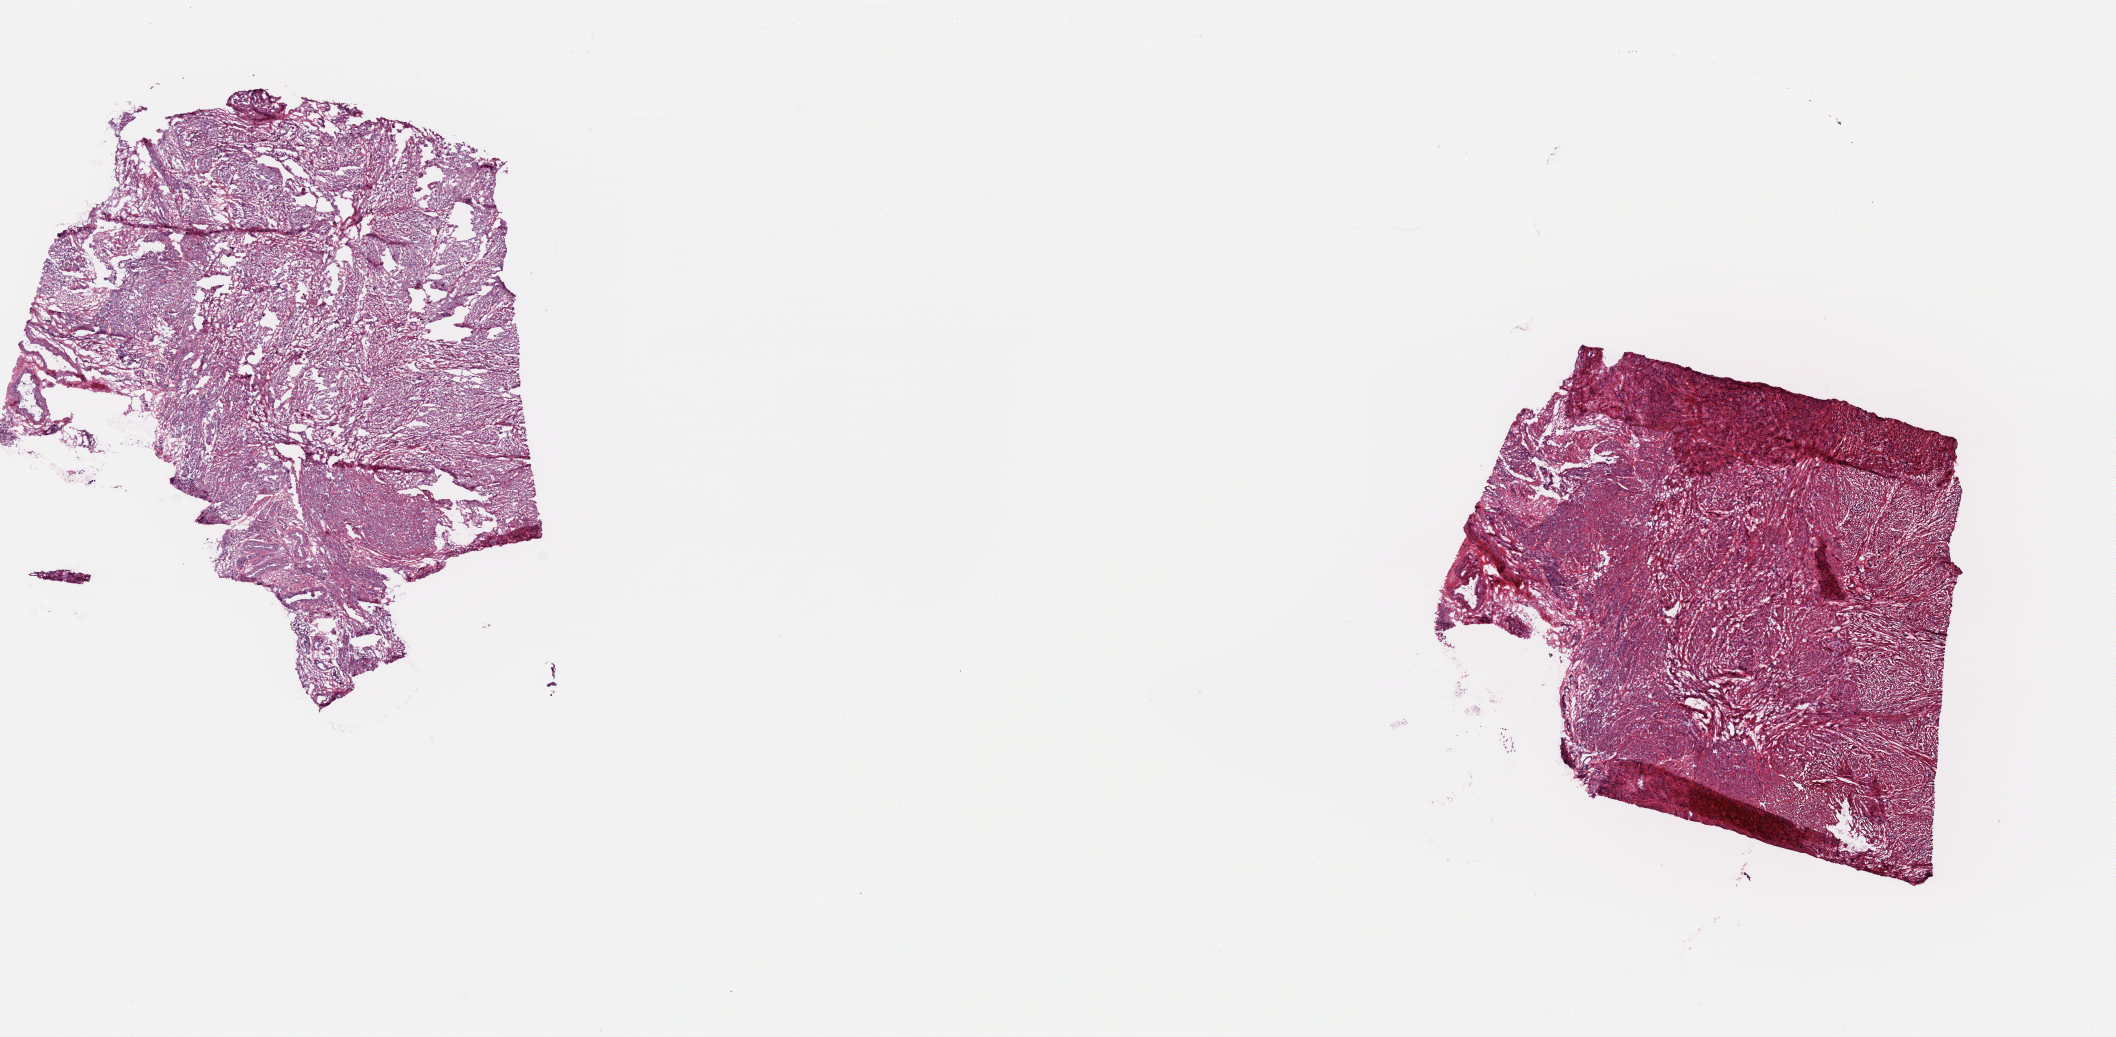
Hematoxylin and eosin (H&E) stained whole-slide image — shown as a low-resolution overview of the whole scanned area (about 16.7 x 8.2 mm), frozen section from the top of the tissue portion, sample: solid tissue normal (non-tumour tissue), uterus. Patient: female, age at initial diagnosis 57 years. Slide review estimates, as recorded: tumour cells 0%, tumour nuclei 0%, normal cells 100%, stromal cells 0%, necrosis 0%. Inflammatory infiltration, as recorded: lymphocyte infiltration 0%, monocyte infiltration 0%, neutrophil infiltration 0%.
This section: solid tissue normal (non-tumour) sample from the same patient. Patient diagnosis: Endometrioid adenocarcinoma, NOS.